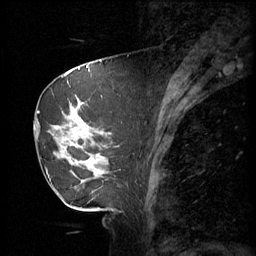
Breast MRI (dynamic contrast-enhanced), one sagittal slice. 3 images stored at this slice position (order not interpretable as contrast timing). 1.5 T. TE 4.2 ms, TR 11 ms. 2 mm slice thickness. 256 × 256 image matrix. Female patient, age 69 years.
Structures marked on this image (semi-automatic segmentation, software-assisted and operator-edited):
- analysis volume of interest (the breast-tissue region the enhancement analysis was run in; not a lesion): bounding box (x1, y1, x2, y2) in pixels: (37, 88, 116, 189)
- tumour enhancement mask (voxels above the 70 % enhancement threshold inside the analysis volume of interest): (56, 100, 103, 183)